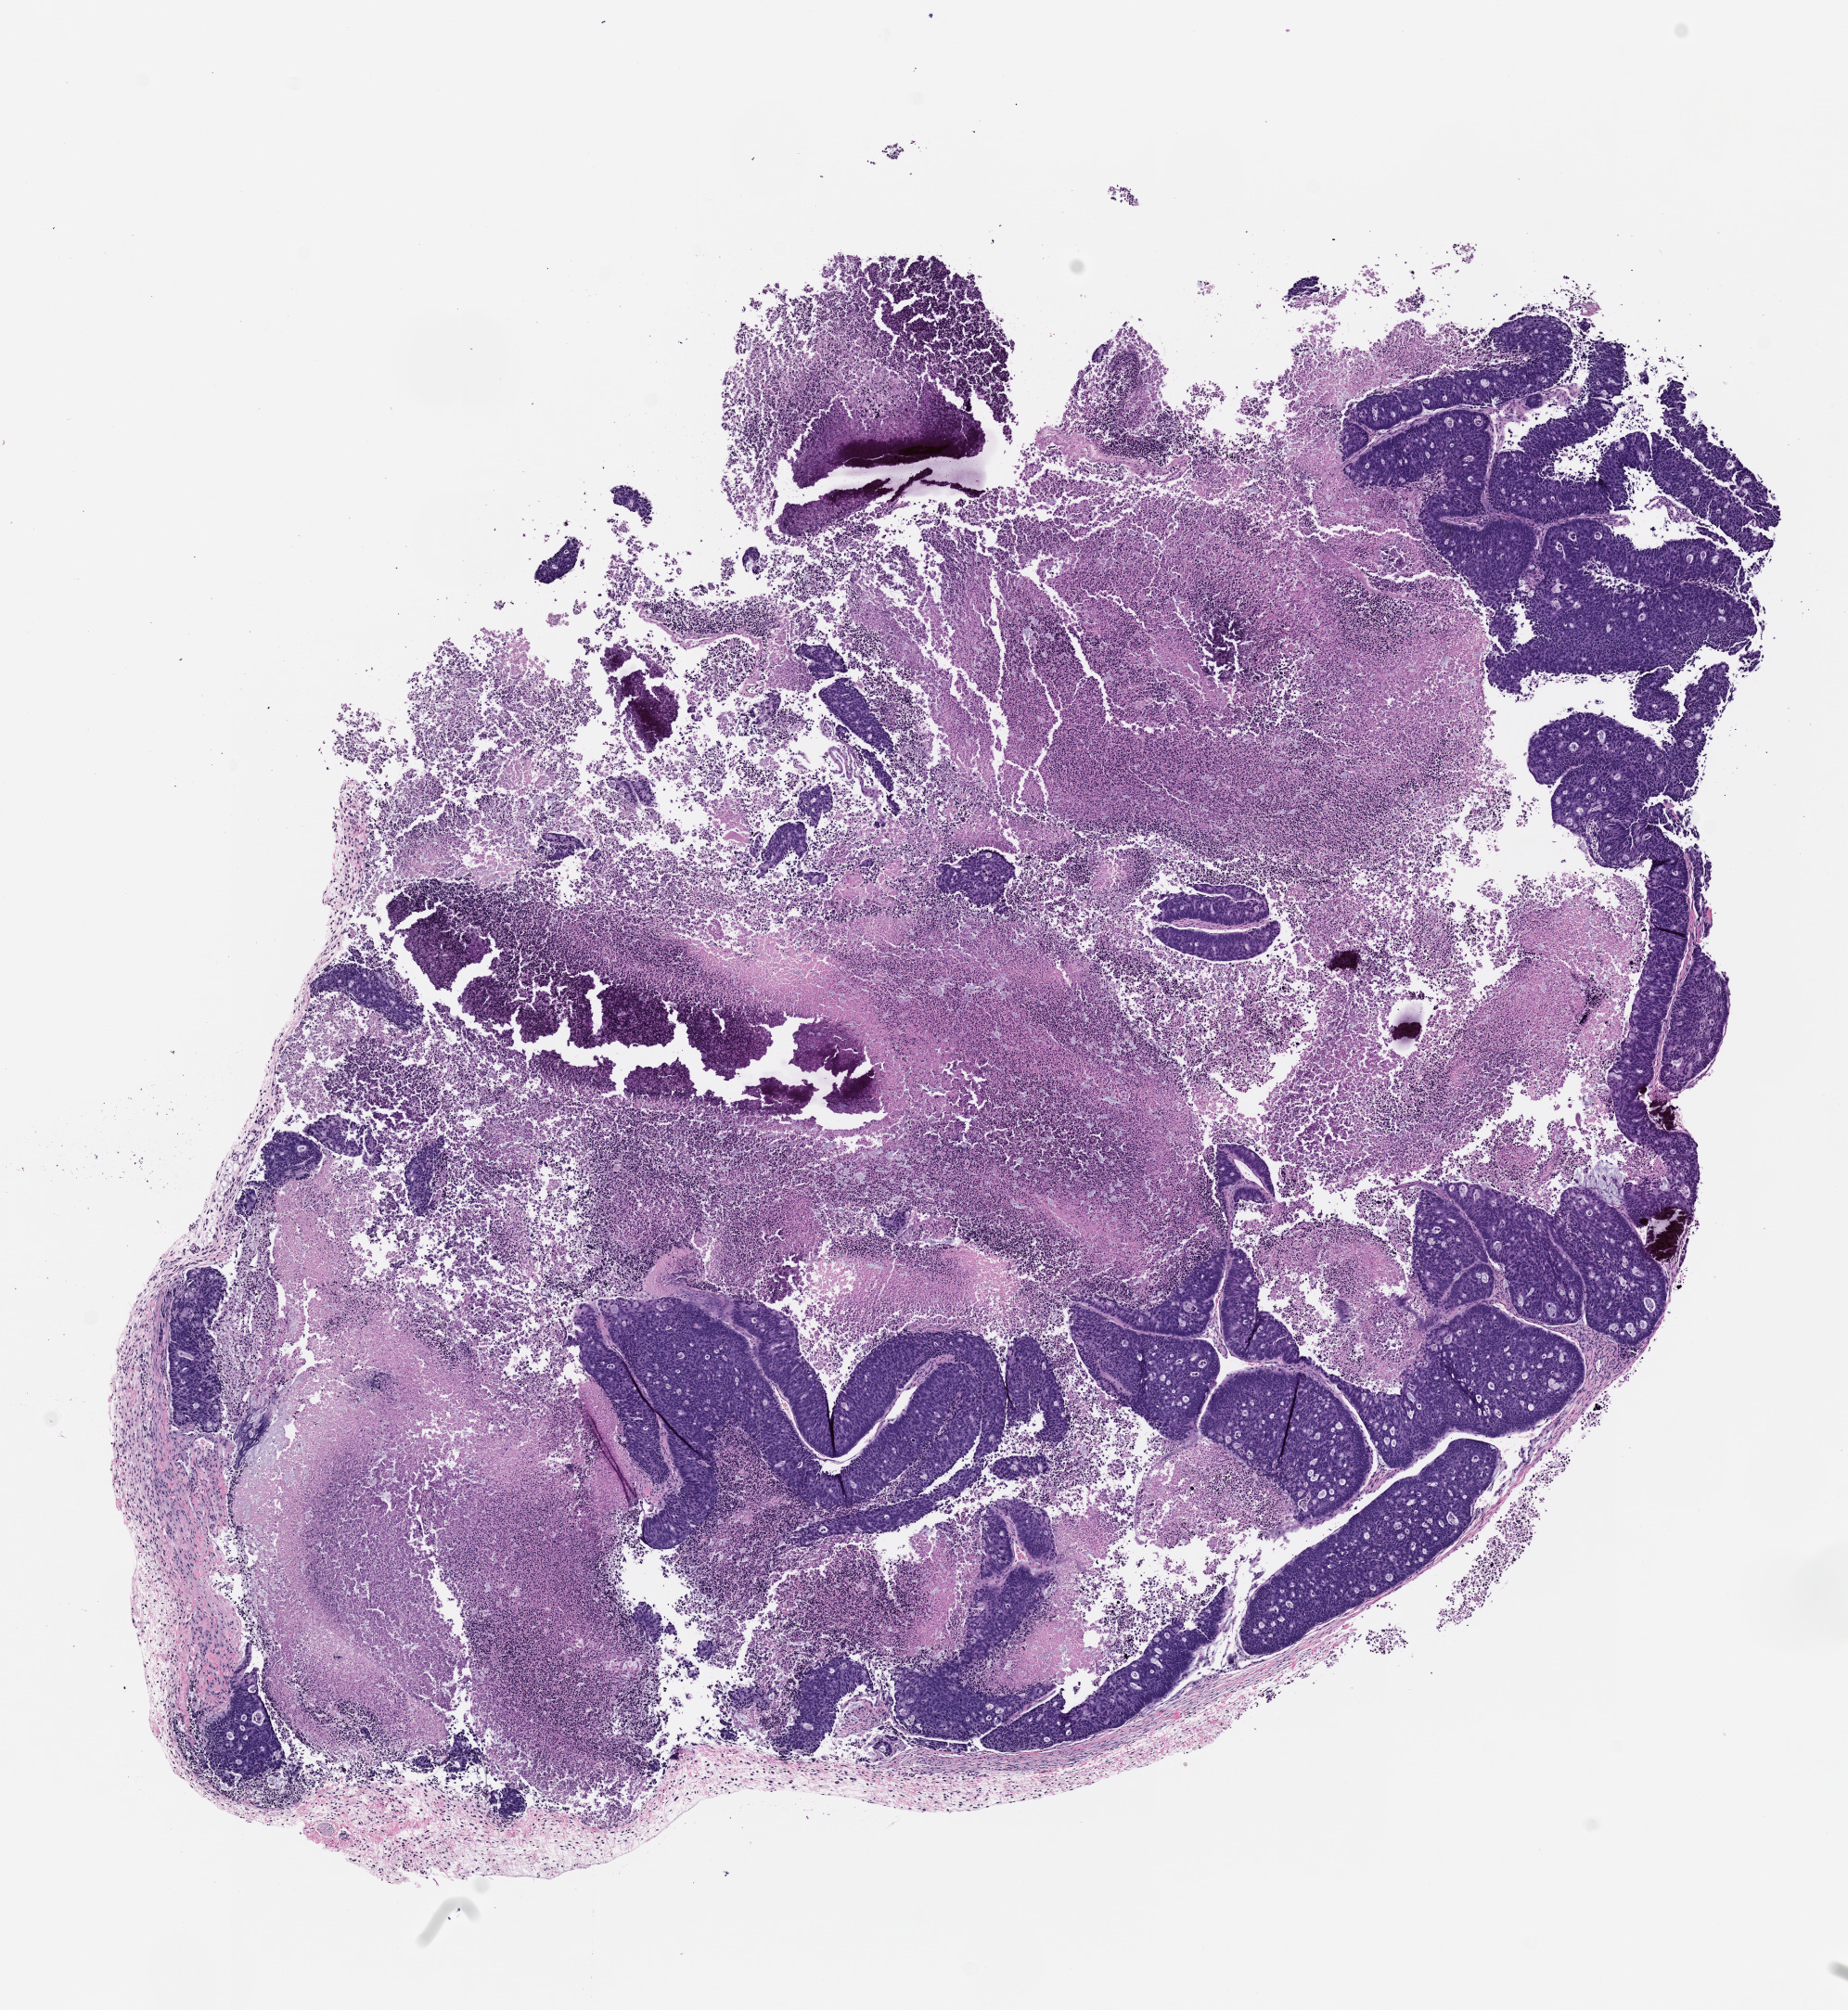
Whole-slide image, H&E: patient-derived xenograft (human tumor grown in a mouse), passage 2 — whole scanned area (about 8.0 x 8.7 mm) shown as a low-resolution overview, FFPE section, originating tumor site category: rectum.
* originating patient diagnosis: Rectal Adenocarcinoma